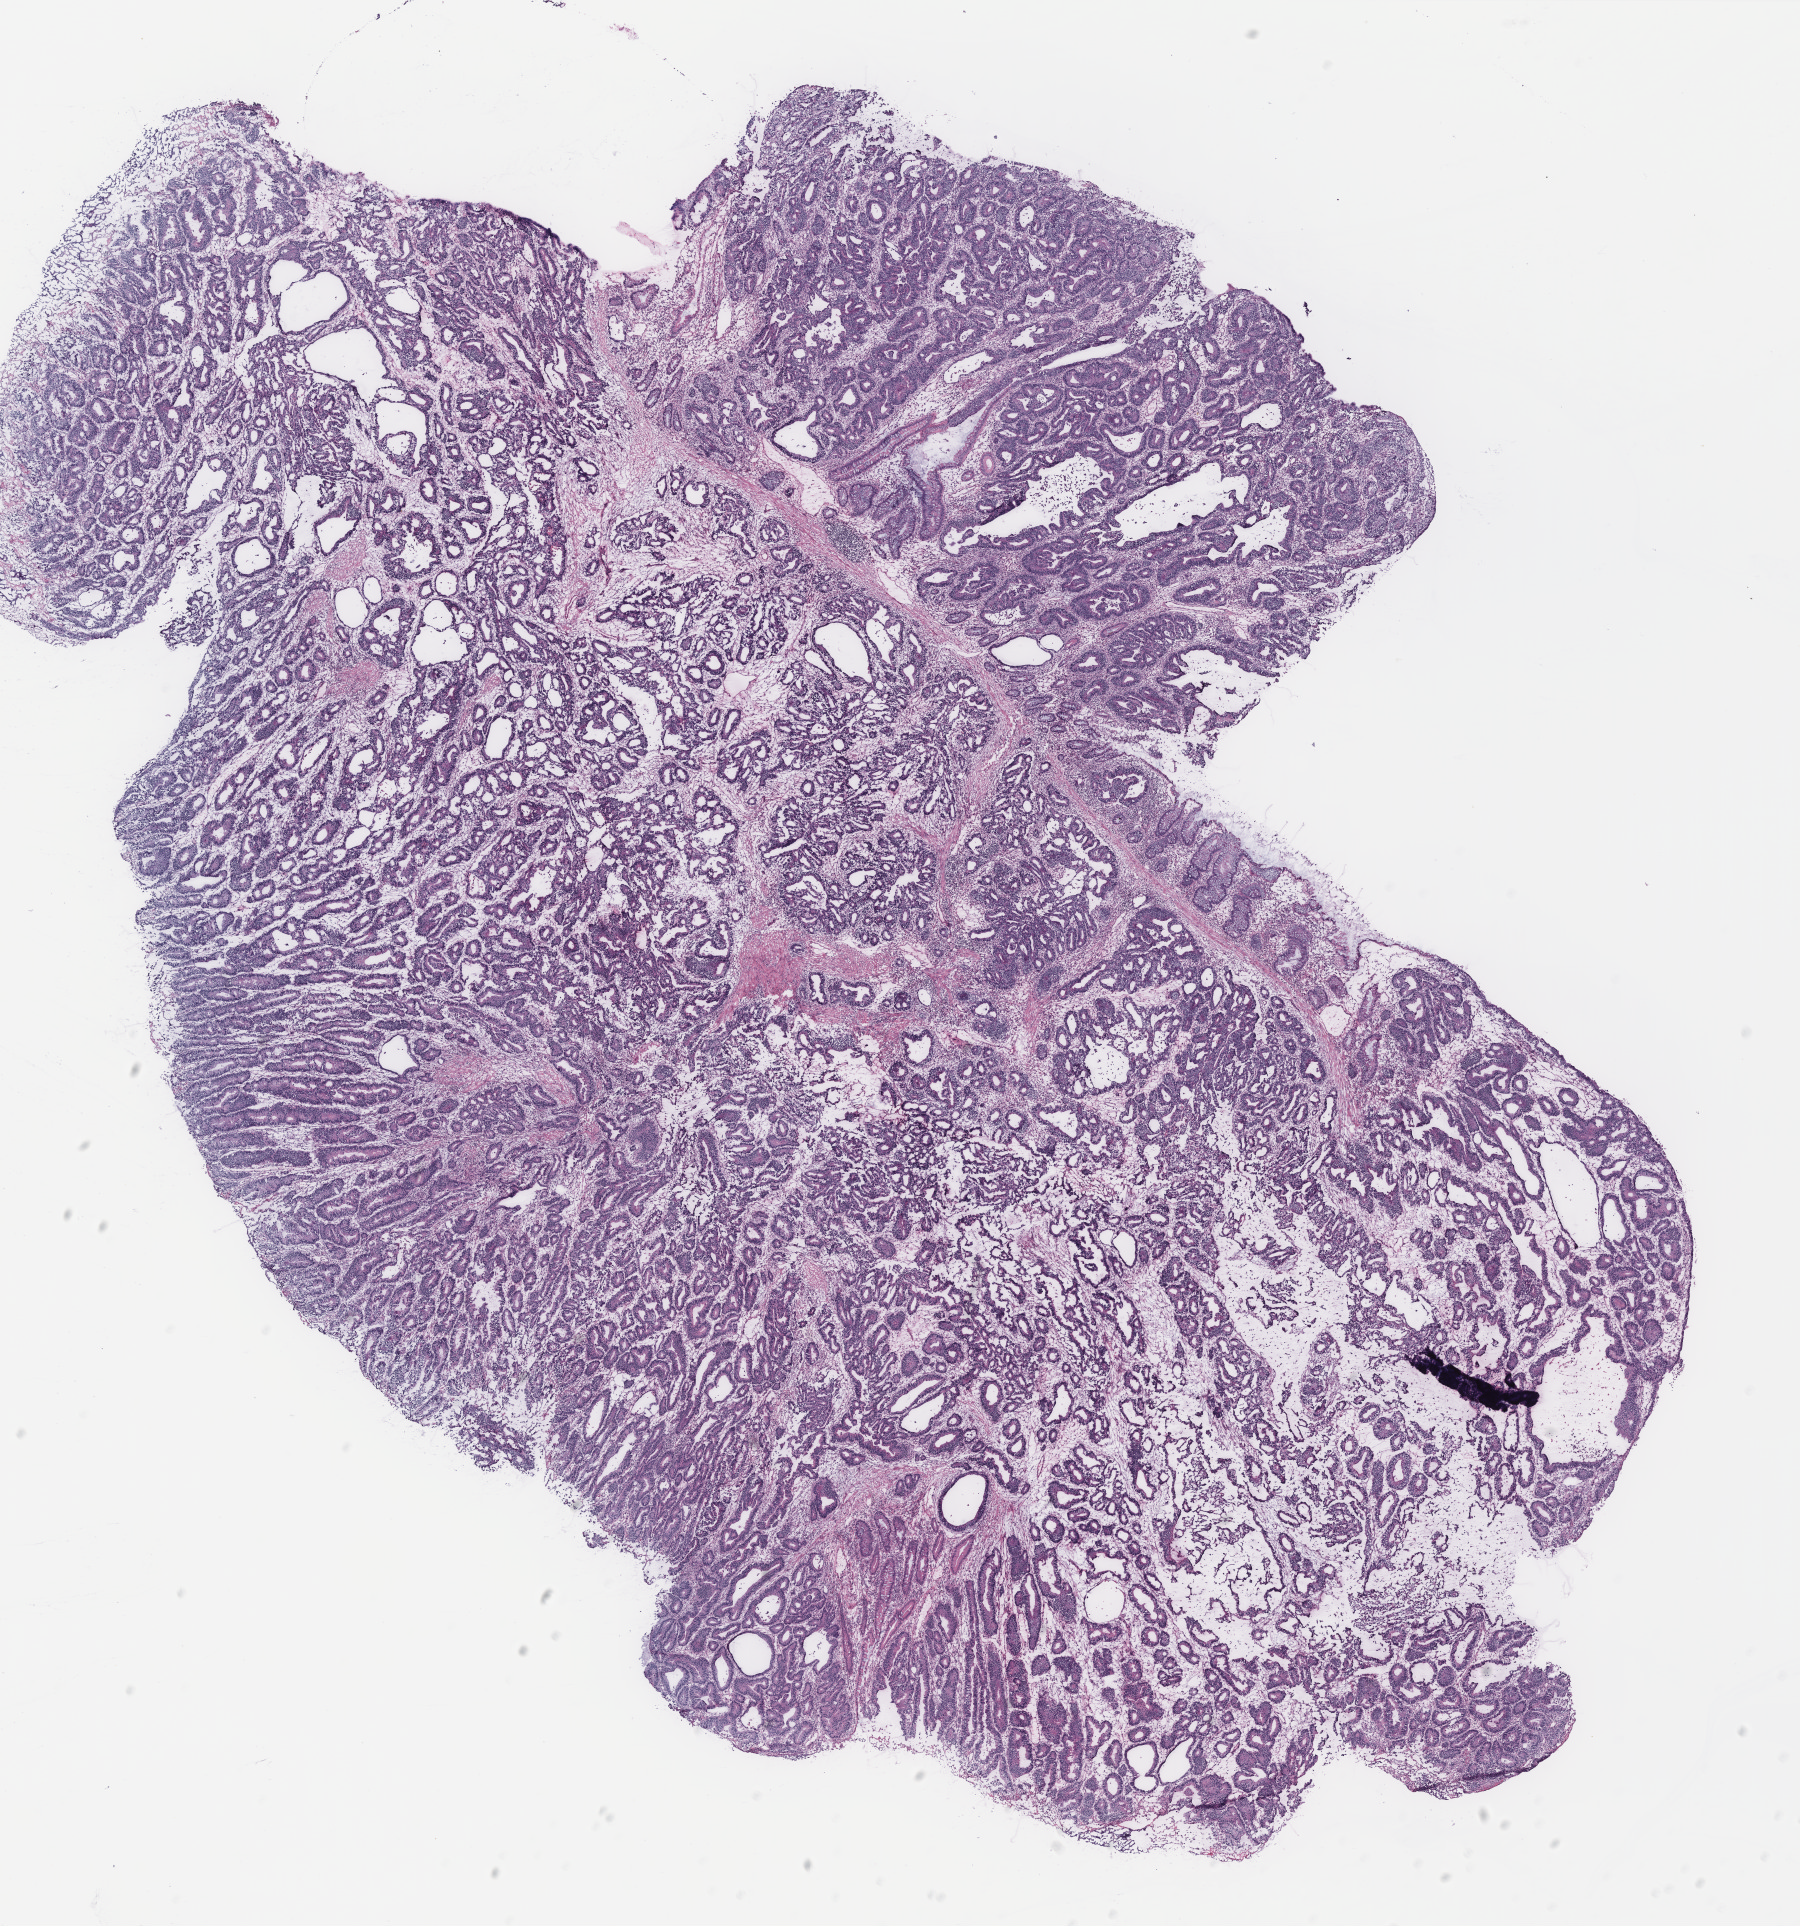
H&E whole-slide image, a low-resolution overview of the entire scanned area, about 14.4 x 15.4 mm (from a 40x scan); colon, tissue type not recorded.
Patient diagnosis (cohort enrolment): colon cancer (colon).